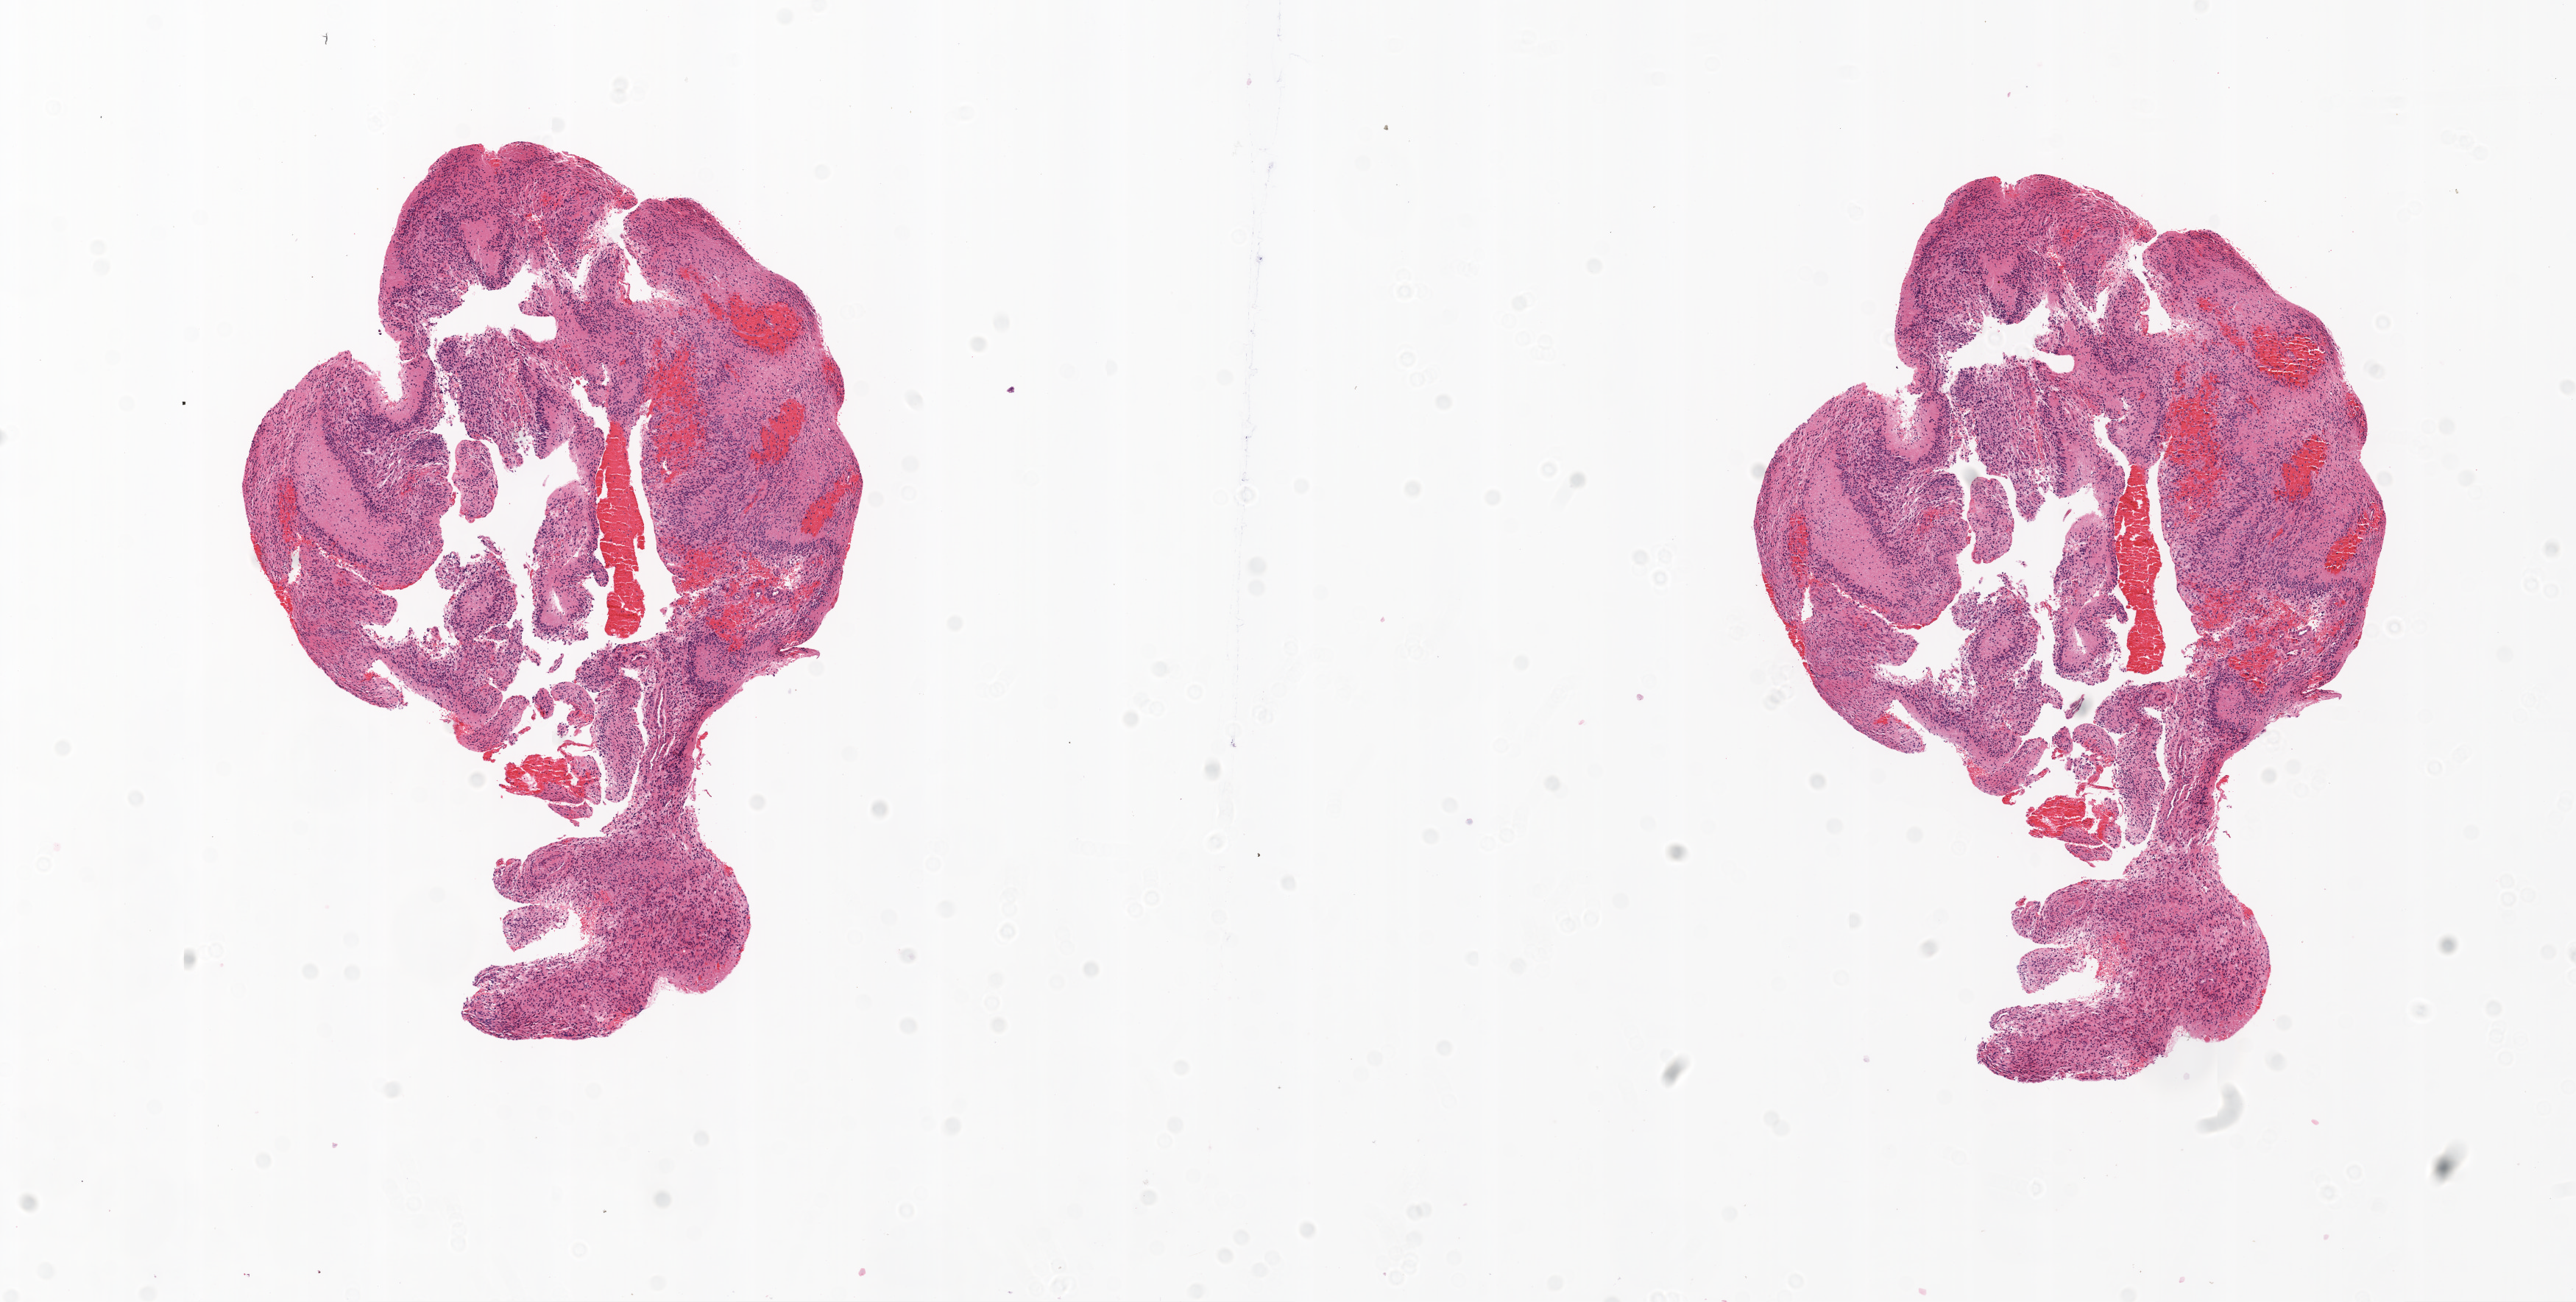
Whole-slide histology image, H&E, a low-resolution overview of the entire scanned area, about 14.0 x 7.1 mm (acquisition: 20x scan); formalin-fixed paraffin-embedded (FFPE) diagnostic section; sample: primary tumour, brain. Male, age 43 years at initial diagnosis.
* diagnosis: Glioblastoma